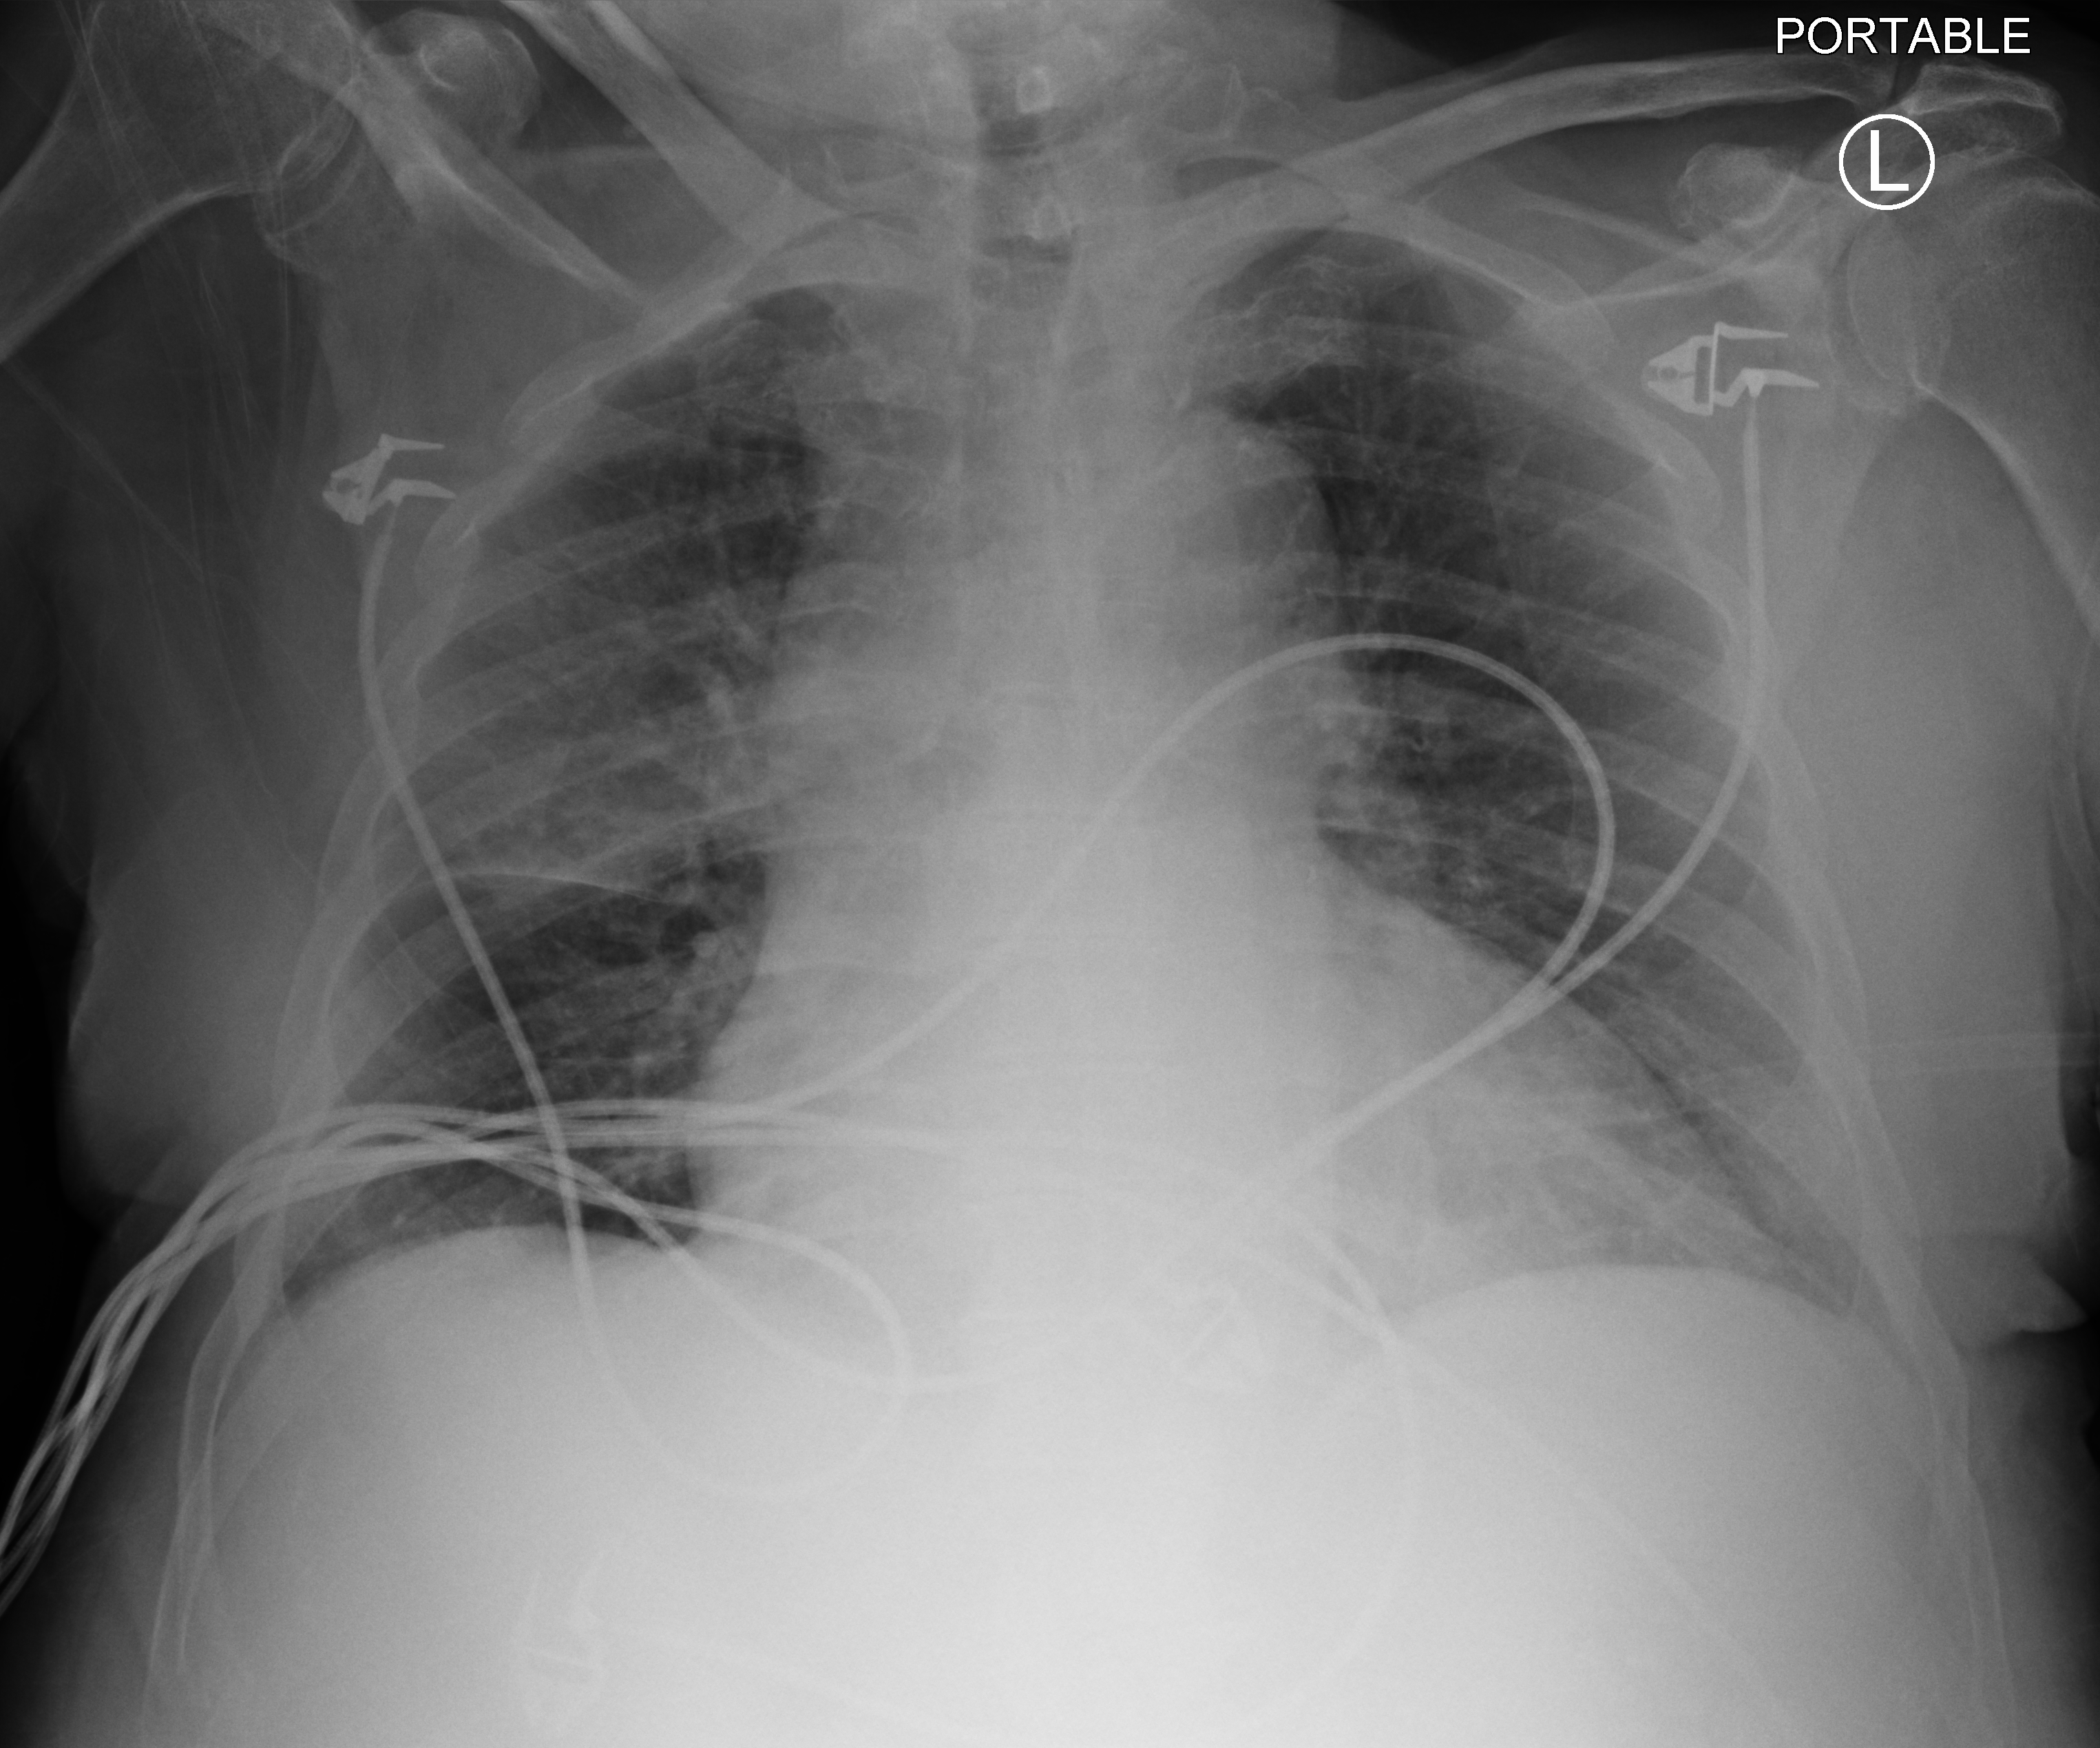
Bedside chest radiograph (computed radiography), anteroposterior (AP) projection. Male patient hospitalised with COVID-19, age 75–90 years.
Admission-level facts for this patient (not findings on this image; timing relative to this image not recorded): chronic kidney disease (admission record): no; mechanically ventilated during this hospital stay: no; admitted to intensive care during this hospital stay: no.